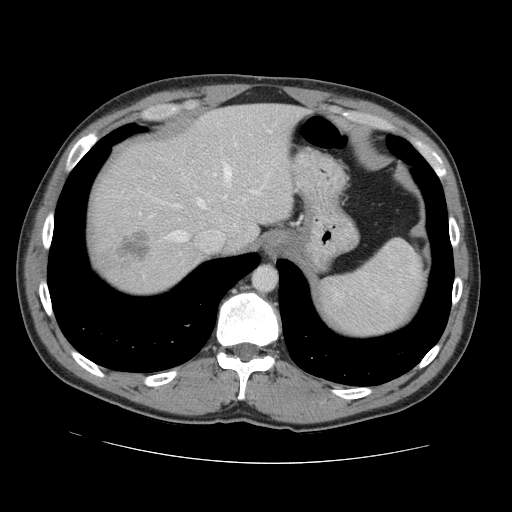
Contrast-enhanced abdominal CT, one axial slice; slice 113 of 131 in the series (ordered by position); intravenous contrast given; soft-tissue window (W 400 / L 40 HU); 2.5 mm slice thickness; 512 × 512 image matrix, field of view 380 × 380 mm. Male patient, age 40 years. Case-level facts recorded for this patient, not image findings: diagnosis: colorectal cancer liver metastases, imaged before liver resection; multiple liver metastases: yes; largest metastasis: 2.9 cm; disease in both lobes: yes.
Structures marked on this image (expert manual segmentation):
- hepatic veins: bounding box [x1, y1, x2, y2] px = [167, 166, 231, 242]
- liver: [89, 104, 301, 292]
- planned liver remnant (the part of the liver to remain after resection): [109, 105, 302, 251]
- portal vein (with intrahepatic branches): [214, 143, 259, 194]
- liver metastasis: [115, 232, 150, 263]